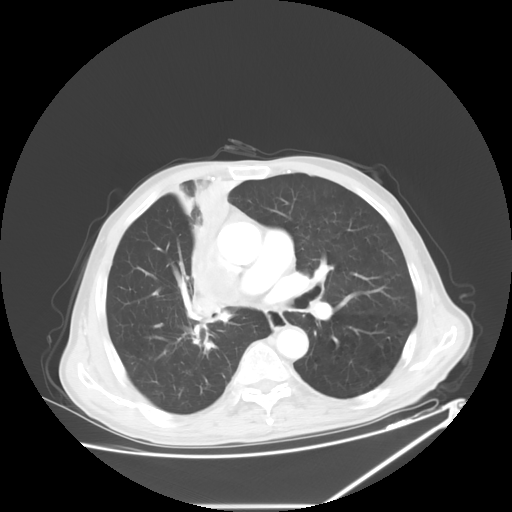
Chest CT, one axial slice. Slice 35 of 60 in the series (ordered by position). 120 kVp. Lung window (W 1500 / L -600 HU). 5 mm slice thickness. 512 × 512 image matrix, field of view 410 × 410 mm. Patient: male, 73 years. Case-level facts recorded for this patient, not image findings: clinical TNM (as recorded): T2a N1 M0.
Structures marked on this image (bounding box drawn by a radiologist):
- lung tumour (recorded histology: squamous cell carcinoma): bounding box (x1, y1, x2, y2) in pixels: (181, 169, 246, 325)